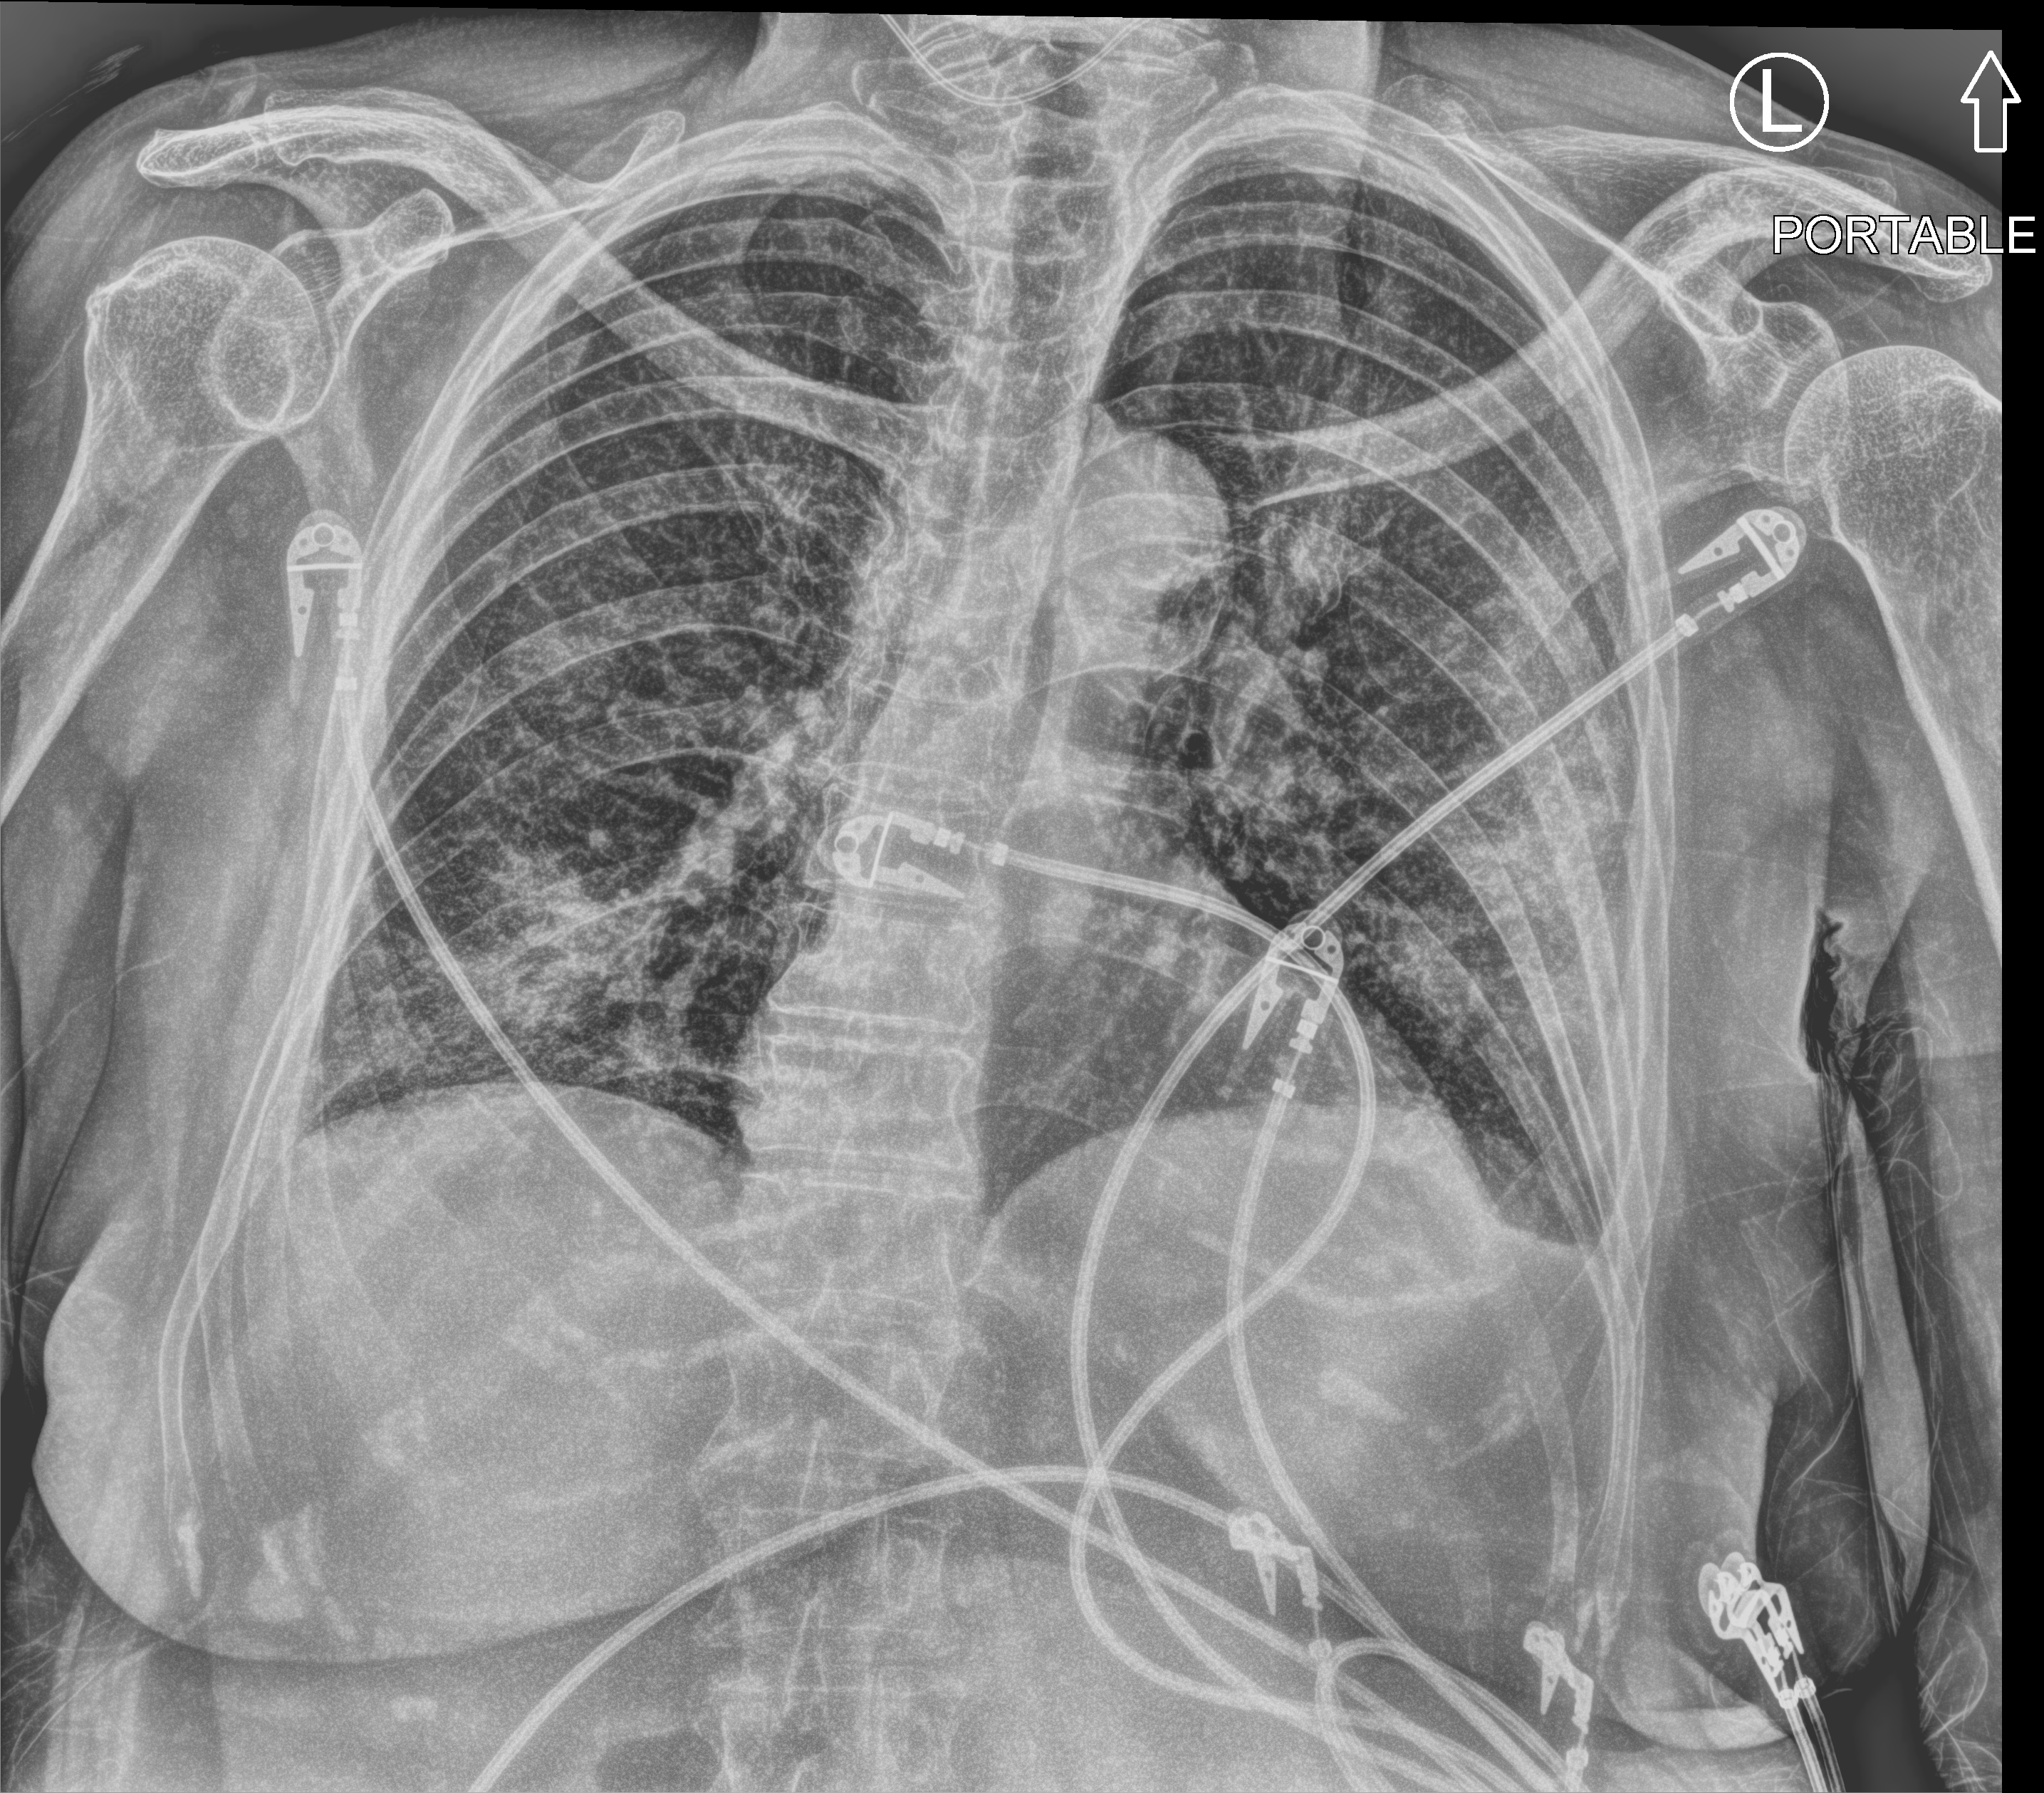
Portable chest radiograph, anteroposterior (AP) projection. Patient hospitalised with COVID-19; female, aged 60–74 years.
From the hospital-stay record, not from the radiograph (when in the stay this image was taken is not recorded): COPD (admission record): no; admitted to intensive care during this hospital stay: no.